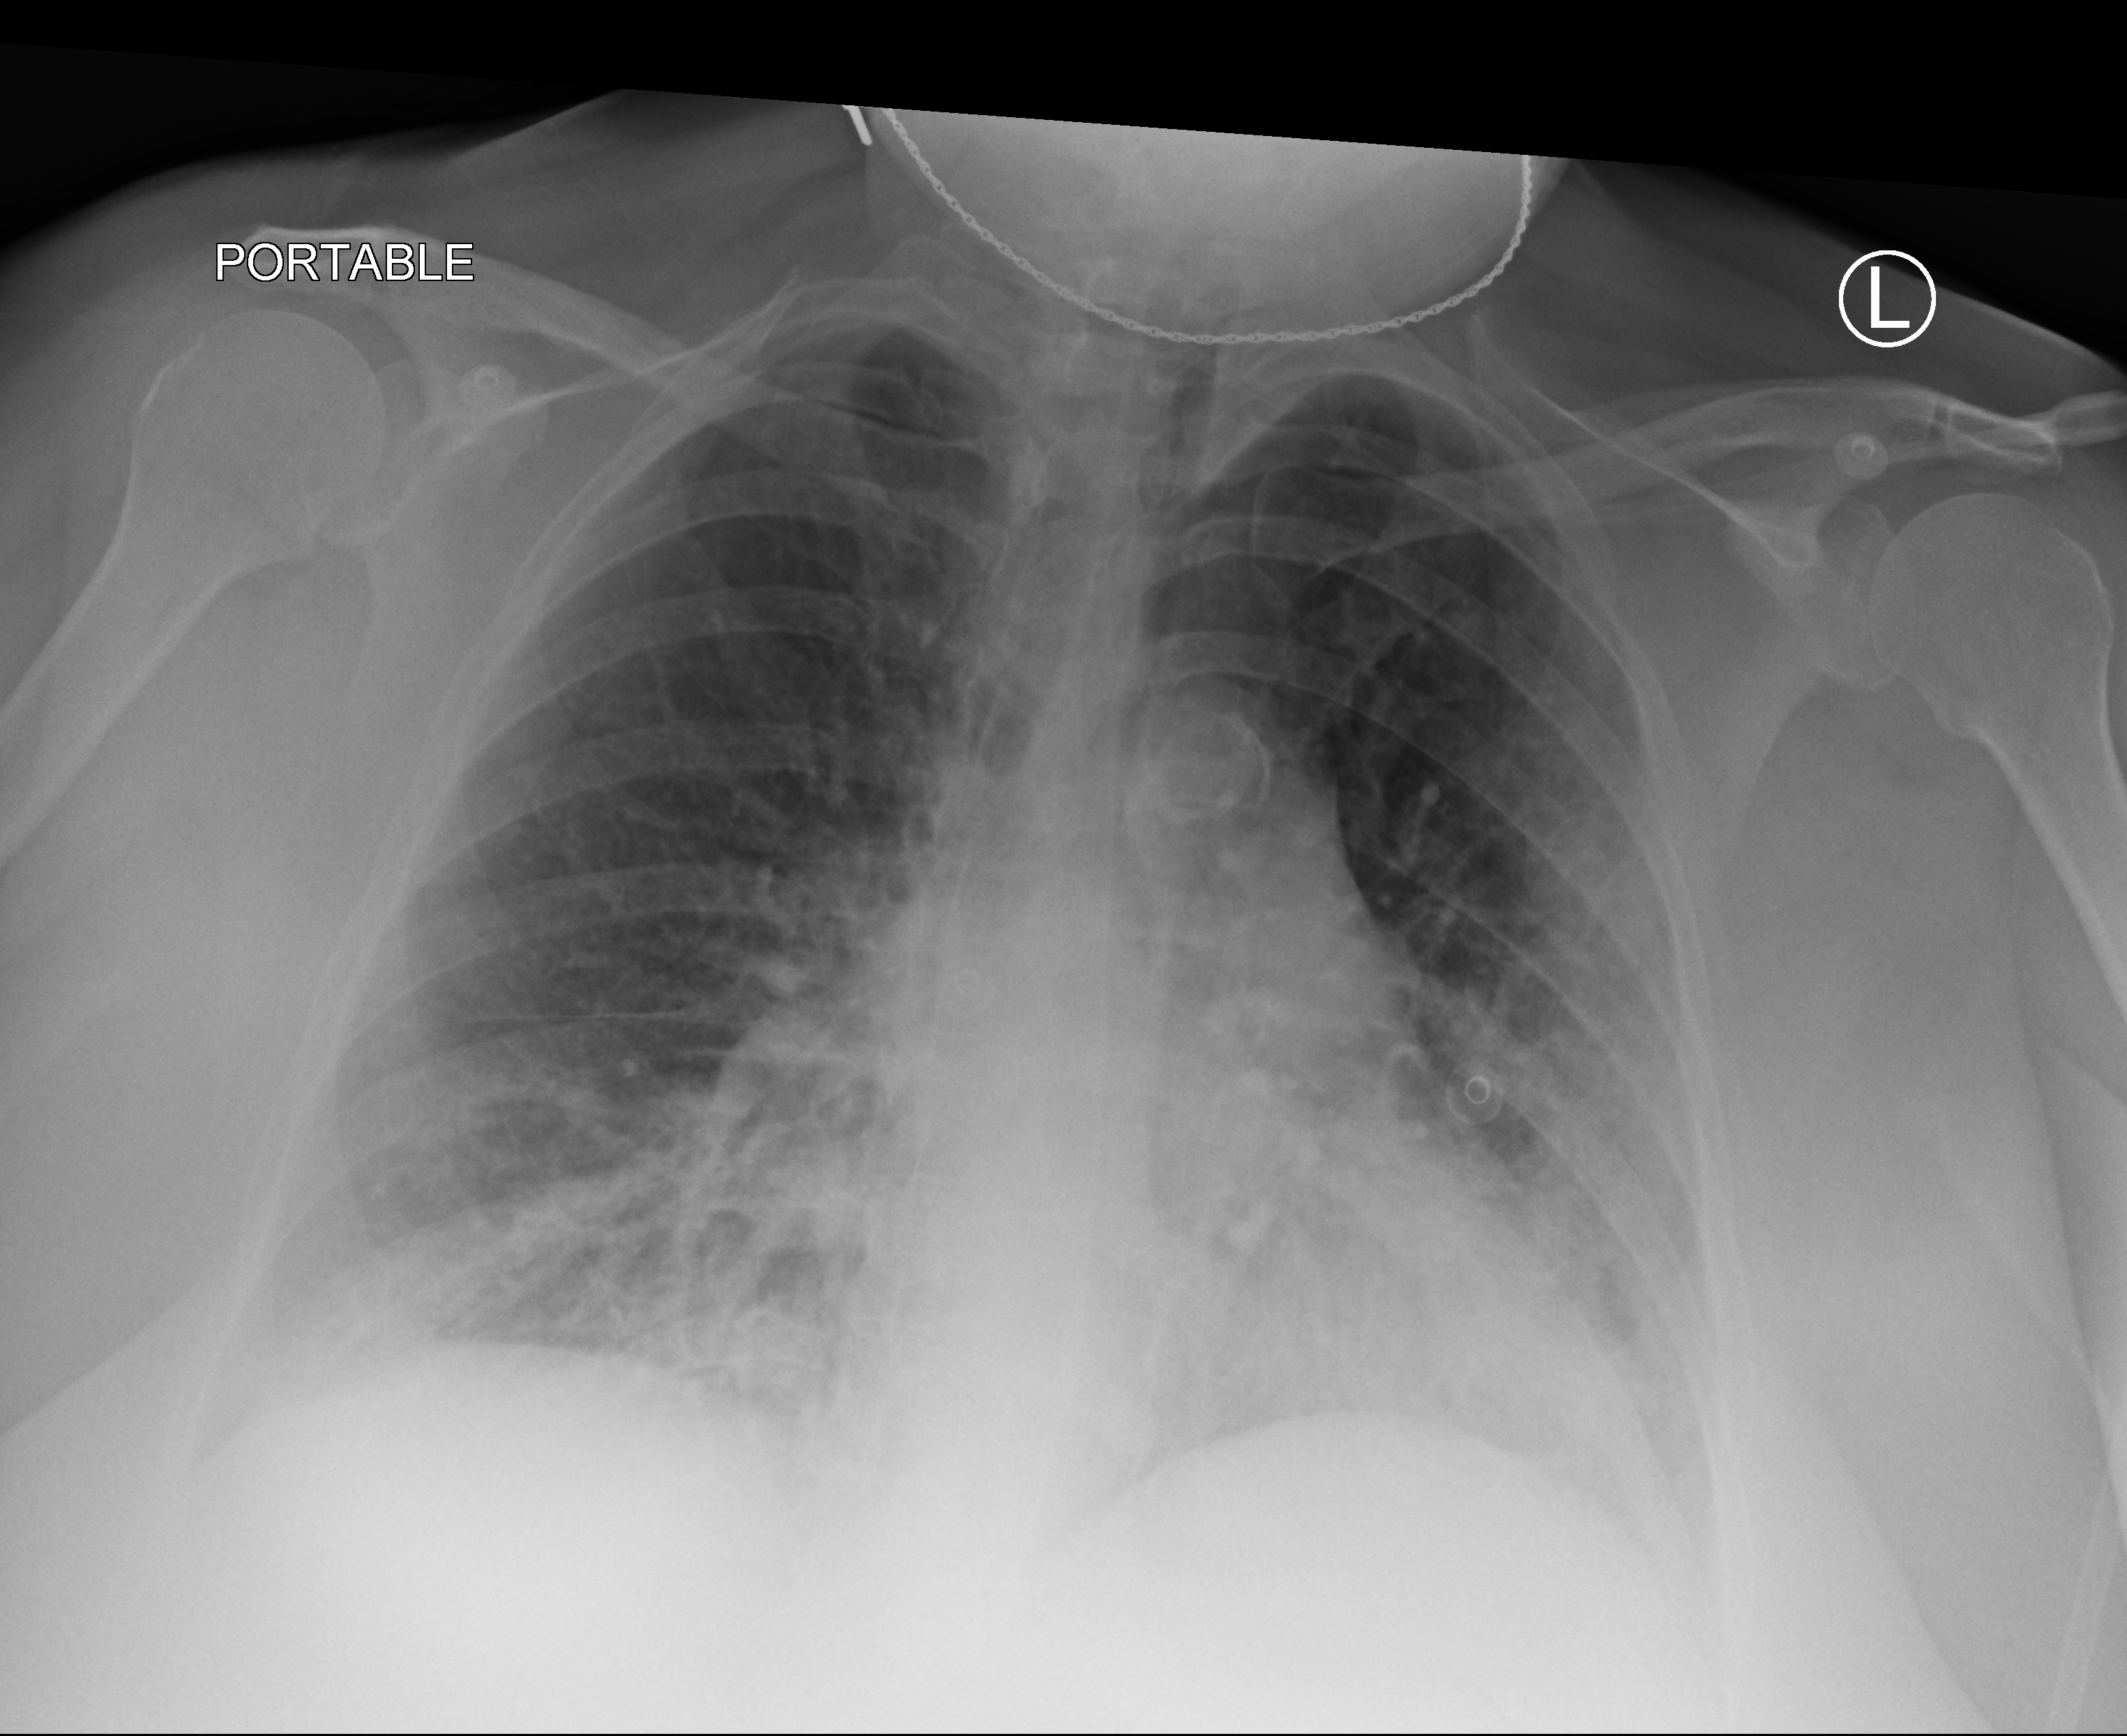
Portable chest radiograph, anteroposterior (AP) projection. Female patient hospitalised with COVID-19, age 60–74 years.
Admission-level facts for this patient (not findings on this image; timing relative to this image not recorded): admitted to intensive care during this hospital stay: no; mechanically ventilated during this hospital stay: no.